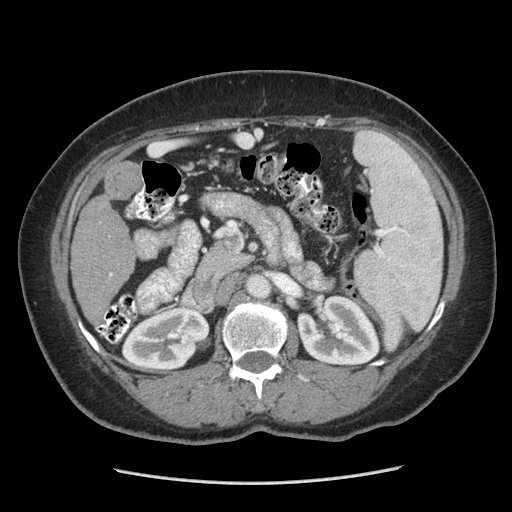
Contrast-enhanced abdominal CT (liver protocol), one axial slice; slice 130 of 185 in the series (ordered by position); reconstruction kernel STANDARD; 140 kVp; soft-tissue window (W 400 / L 40 HU); 2.5 mm slice thickness; 512 × 512 image matrix, field of view 360 × 360 mm. From the clinical record (not read from this slice): diagnosis: hepatocellular carcinoma (patient treated with transarterial chemoembolisation; whether this scan precedes or follows treatment is not stated here); TNM stage (as recorded): Stage-I; Child-Pugh class: A; tumour differentiation: poorly differentiated; tumour nodularity: uninodular.
Structures marked on this image (semi-automatic segmentation, software-assisted and operator-edited):
- liver parenchyma outside the tumour (the mass and vessels are separate outlines, so this box may not span the whole liver): bounding box <70,162,136,316> (left, top, right, bottom; pixels)
- mass: <106,164,140,198>
- liver vessels: <110,273,112,276>